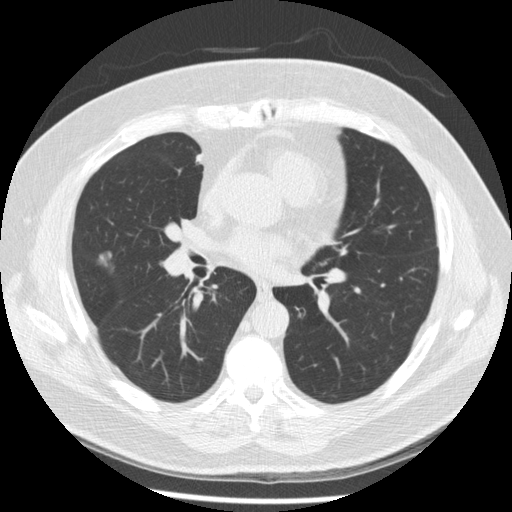
Axial slice from a low-dose chest CT screening exam, second annual screen, lung window (W 1500 / L -600 HU), slice 114 of 230 in the series, 512 × 512 image matrix. Male, age 67 years at enrolment. Former smoker at enrolment.
Expert reader's lesion annotation, bounding box [x1, y1, x2, y2] px = [83, 245, 123, 288]. Reader record for this screening exam (exam-level; its link to the box is not recorded): non-calcified nodule or mass ≥4 mm, right middle lobe, 19 × 16 mm, smooth margins, soft tissue attenuation, pre-existing on the prior screen: yes; interval growth: yes. Official screen result: positive, other. Later outcome: lung cancer diagnosed 47 days after this screen — adenocarcinoma, NOS, right middle lobe, moderately differentiated (G2), stage IA (AJCC 6th edition), 14 mm at pathology.